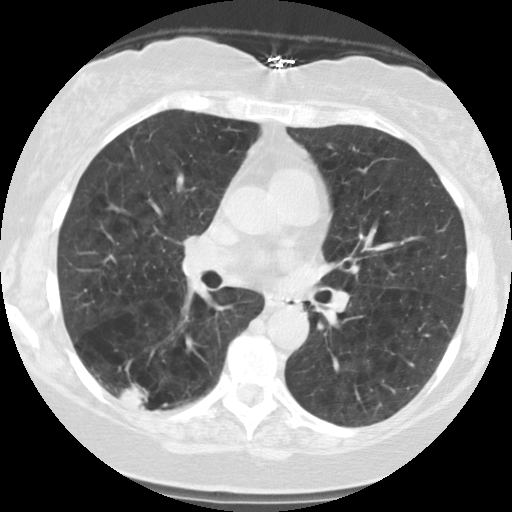
Low-dose screening chest CT, one axial slice. Position 62 of 122 along the scan axis. Reconstruction kernel STANDARD. Lung window (W 1500 / L -600 HU). 2.5 mm slice thickness. 512 × 512 image matrix, field of view 310 × 310 mm.
Outlined on this slice (expert manual segmentation):
- lesion 1 (tumor, lower lobe of right lung): bounding box [x1, y1, x2, y2] px = [118, 383, 148, 409]